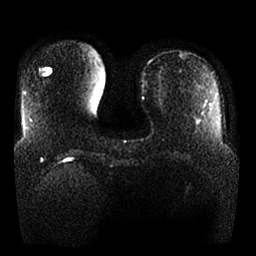
Breast MRI, one axial slice. Position 6 of 25 along the scan axis. Diffusion-weighted series; image 2 of 4 stored at this slice position (different b-values; order by instance number). 1.5 T. 4 mm slice thickness. 256 × 256 image matrix, field of view 360 × 360 mm. Female patient.
Structures marked on this image (manually delineated by an expert):
- tumour on diffusion-weighted imaging: bounding box (x1, y1, x2, y2) in pixels: (42, 69, 51, 74)